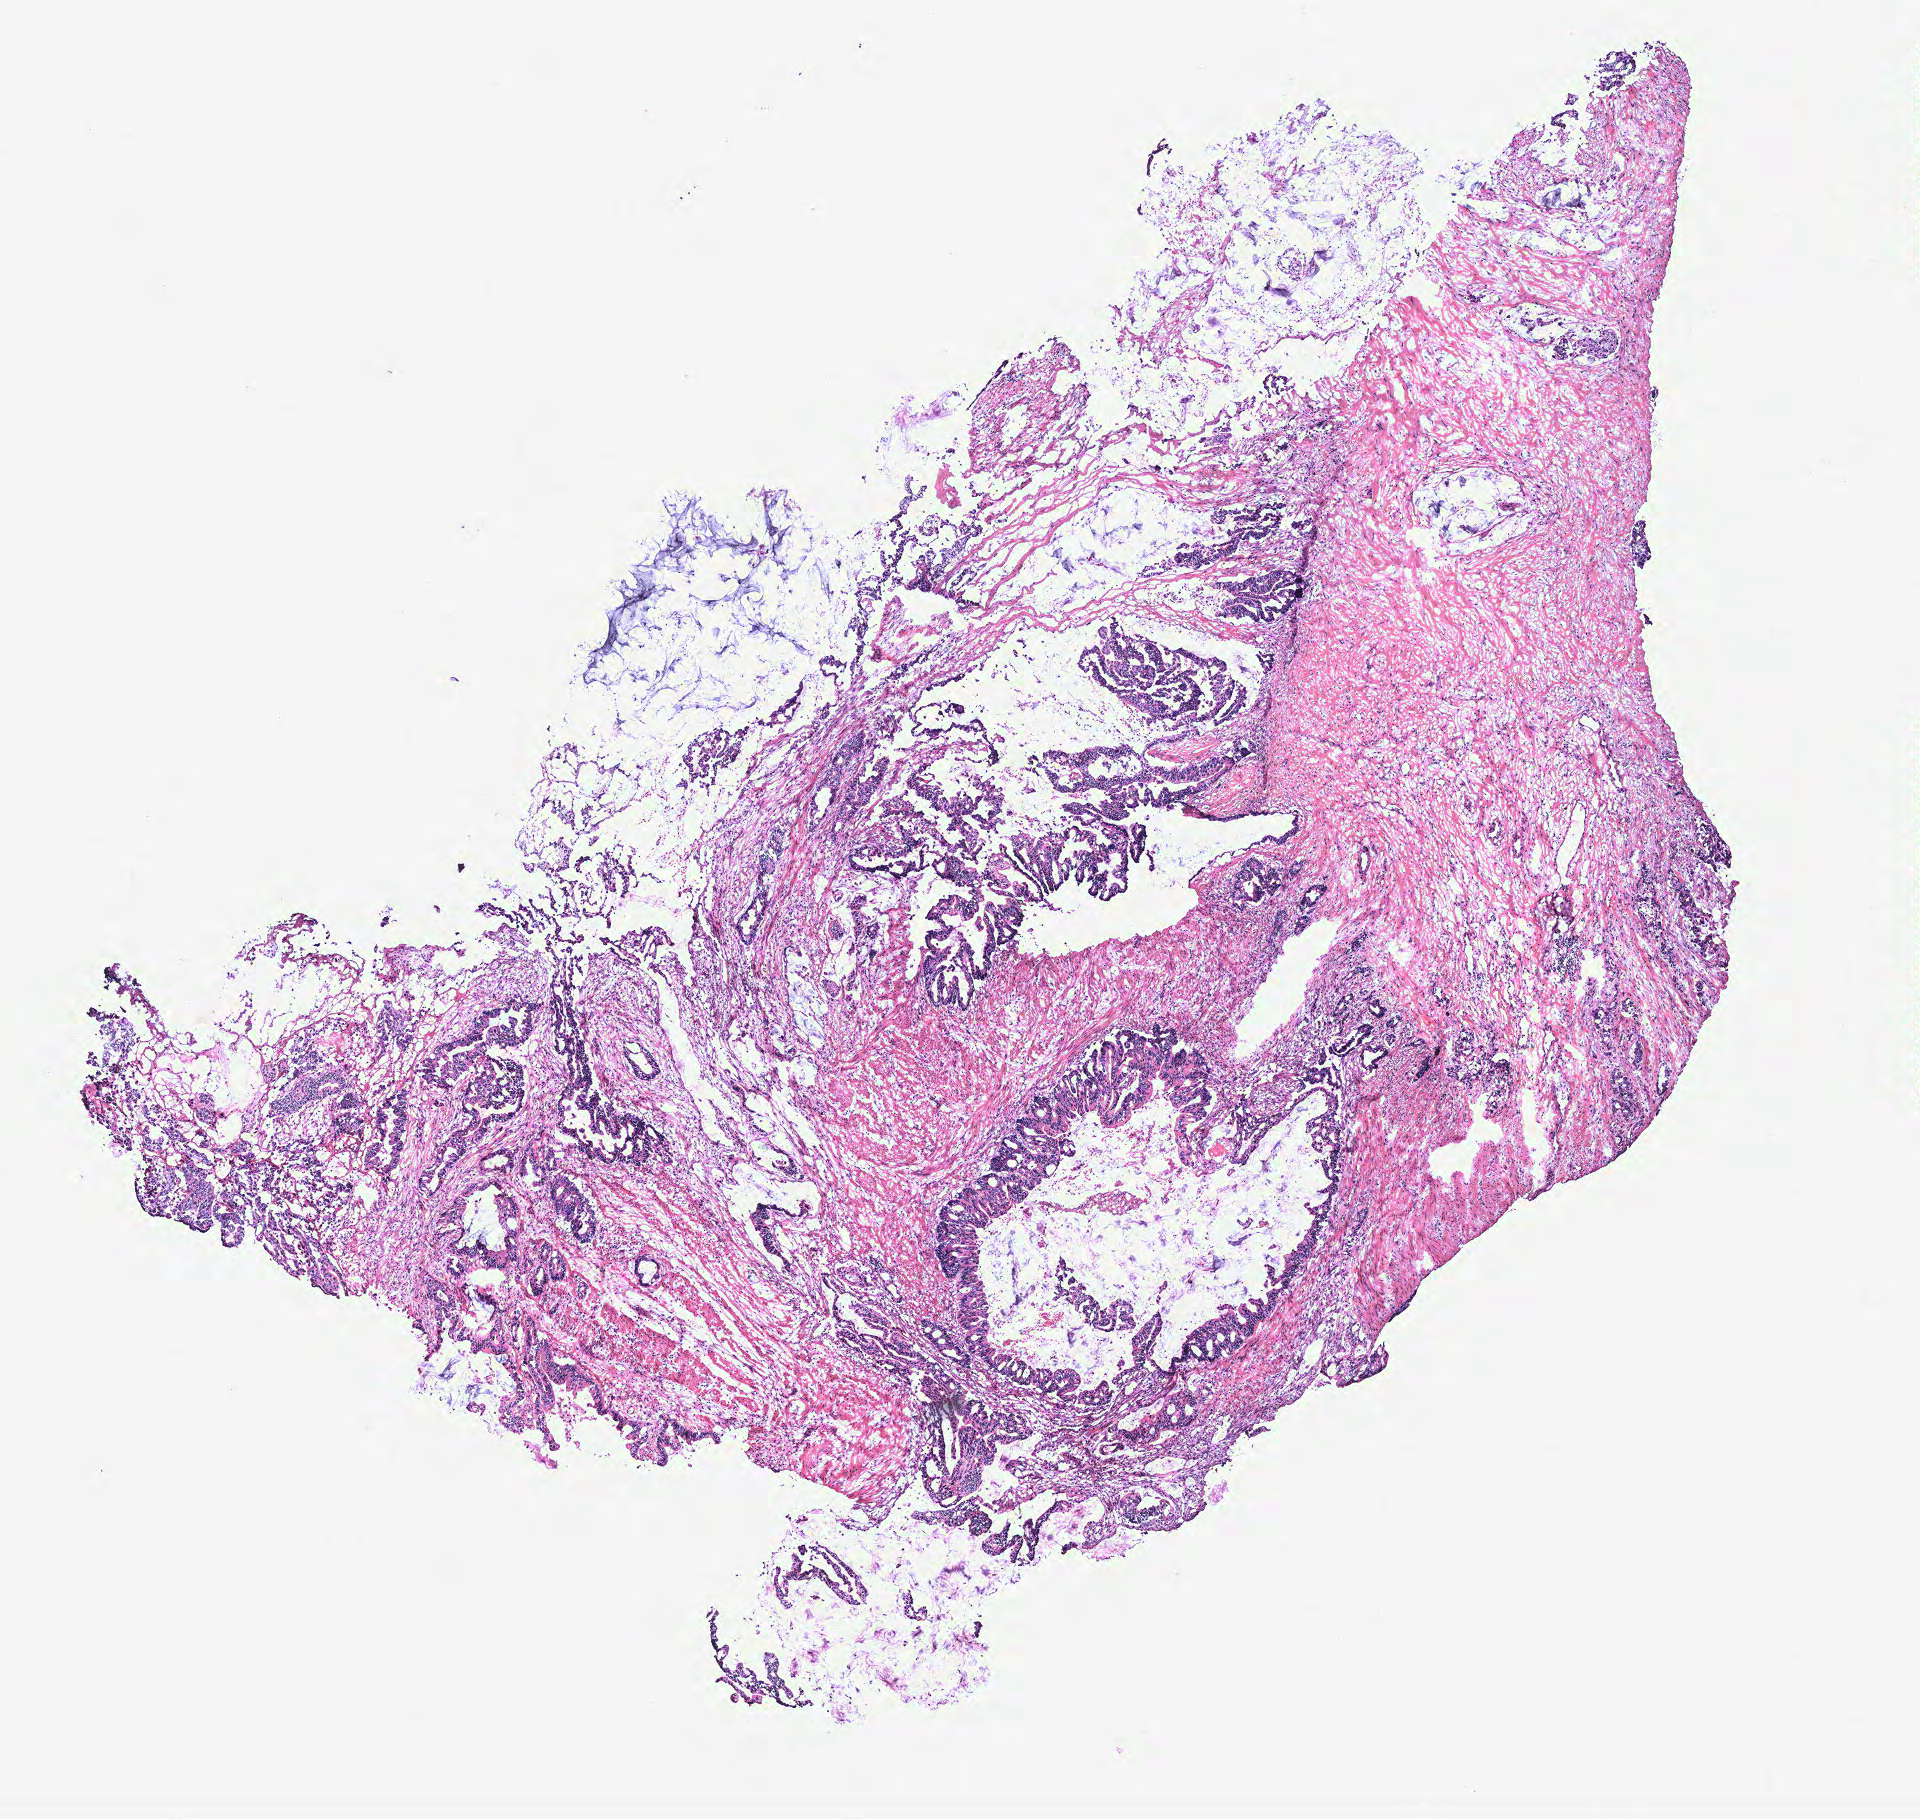
Digitized H&E tissue section (whole slide) — a low-resolution overview of the entire scanned area, about 7.7 x 7.3 mm; colon, tissue type not recorded.
- patient diagnosis (cohort enrolment): colon cancer (colon)